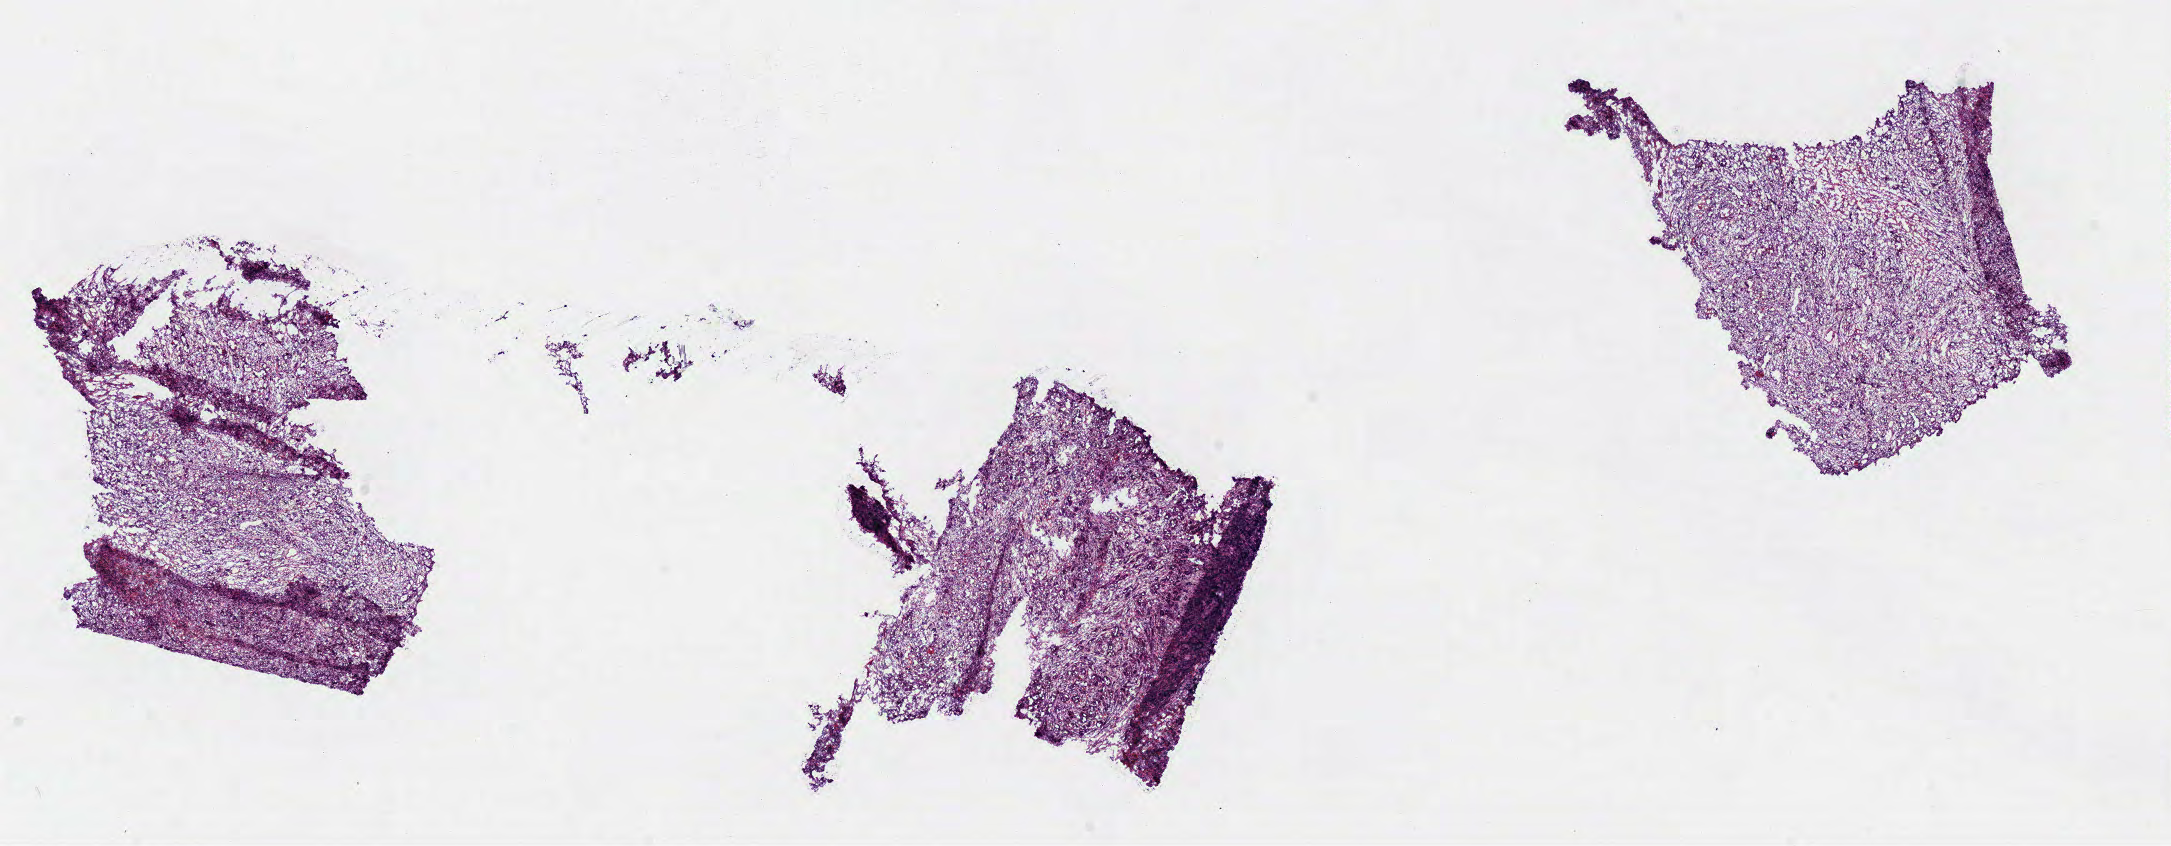
Whole-slide histology image, Hematoxylin and eosin (H&E) stained, shown as a low-resolution overview of the whole scanned area (about 17.1 x 6.7 mm, acquisition: 40x scan), frozen section from the bottom of the tissue portion, primary tumour sample from the head and neck. Female, age 63 years at initial diagnosis. Slide review estimates, as recorded: tumour cells 90%, tumour nuclei 80%.
Histologic diagnosis: Squamous cell carcinoma, NOS (overlapping lesion of lip, oral cavity and pharynx).